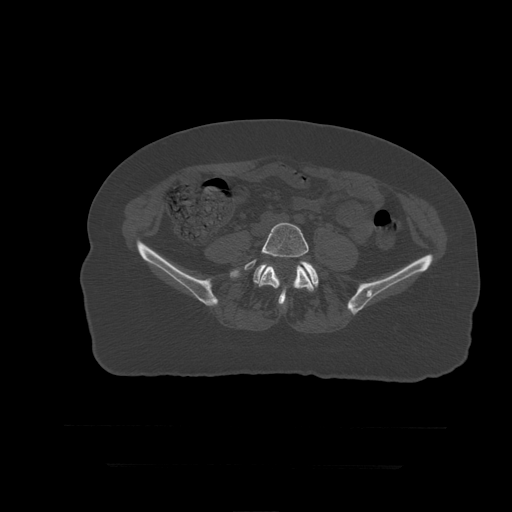
CT including the spine, one axial slice; position 69 of 399 along the scan axis; 120 kVp; bone window (W 1800 / L 400 HU); 1.25 mm slice thickness; 512 × 512 image matrix, field of view 450 × 450 mm. Patient age 41 years. Case-level facts recorded for this patient, not image findings: primary cancer: breast.
Structures marked on this image (semi-automatically segmented with operator editing):
- L5 vertebra: bounding box [x1, y1, x2, y2] px = [244, 223, 316, 306]